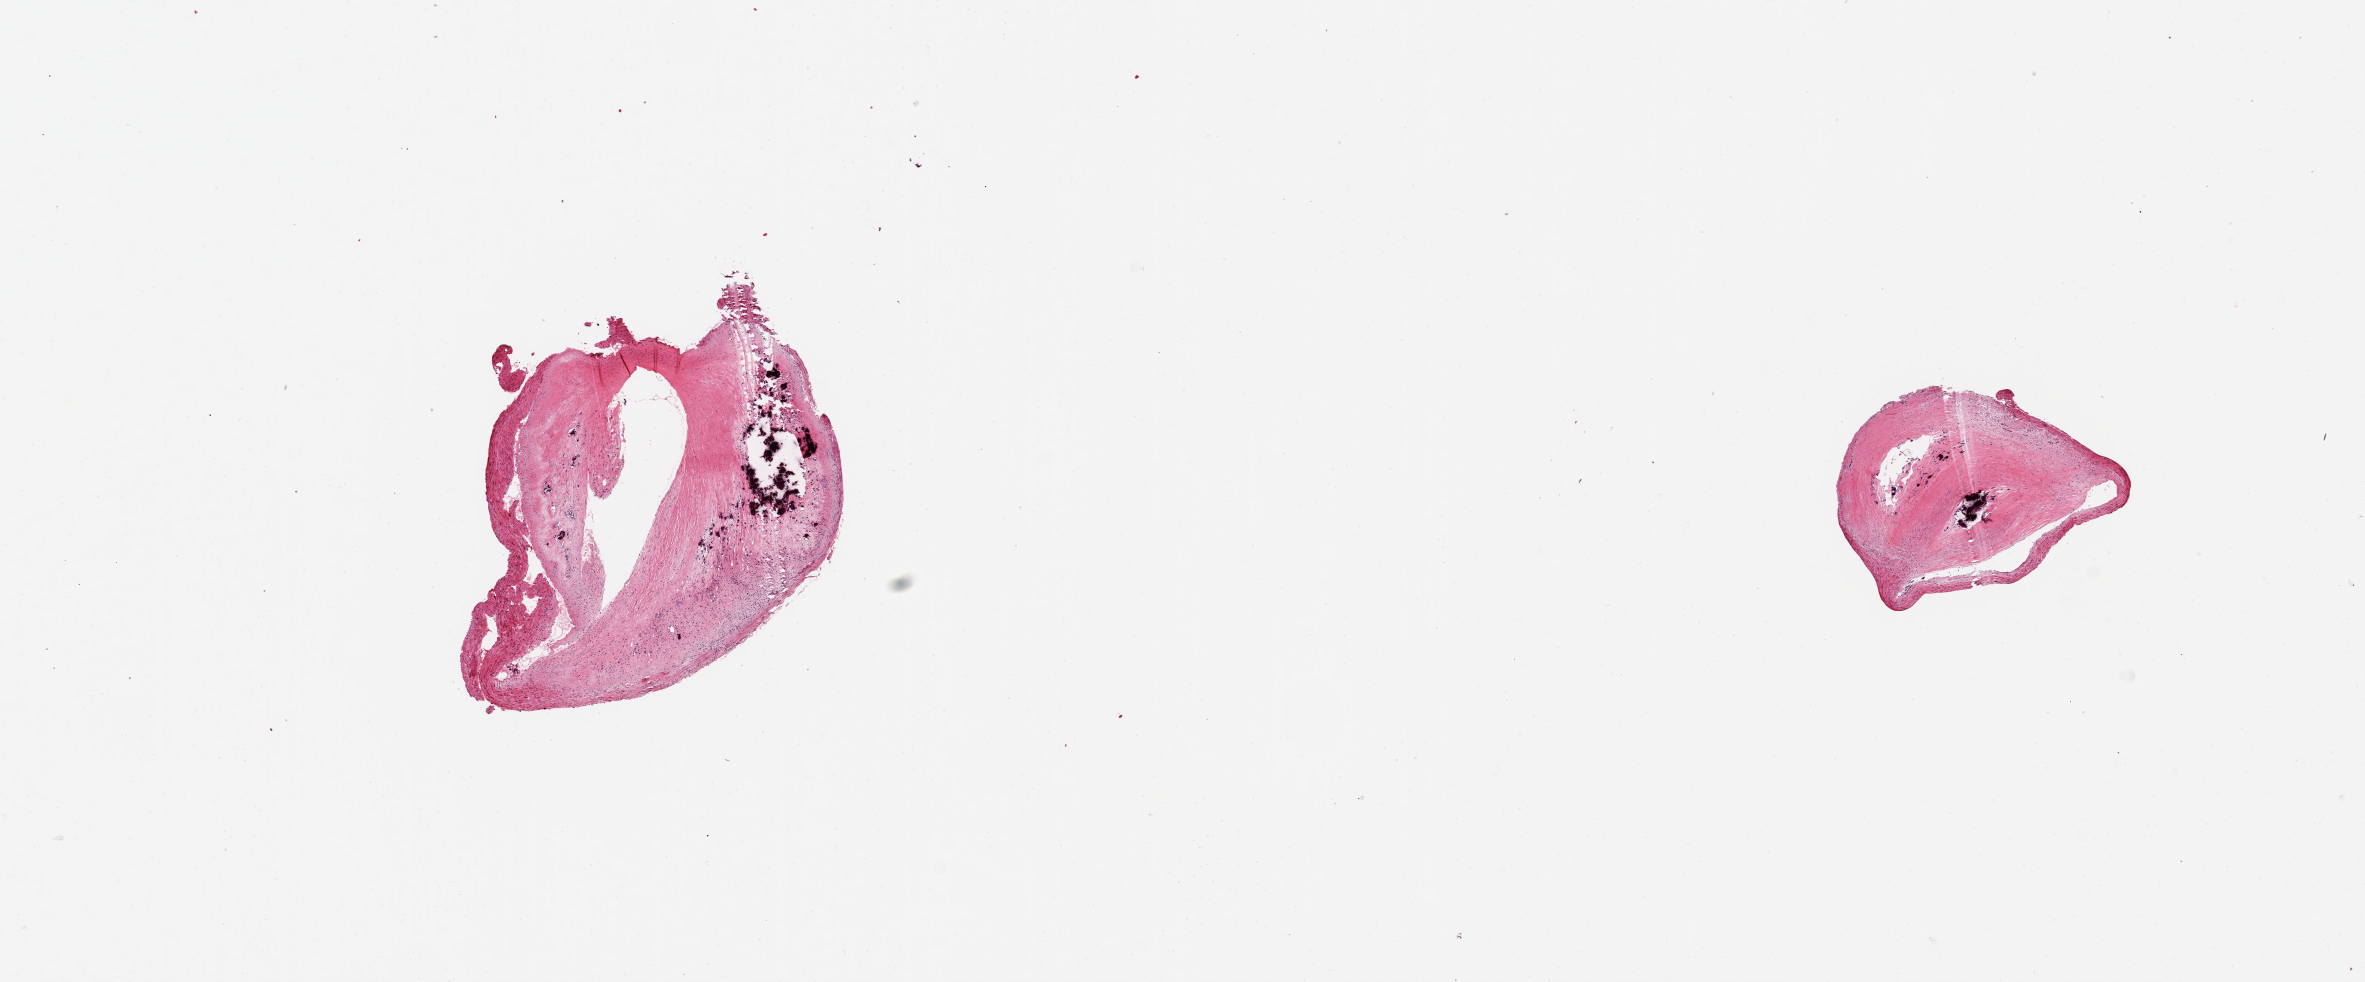
Whole-slide image, H&E stain, a low-resolution overview of the entire scanned area, about 18.7 x 7.8 mm. PAXgene-fixed, paraffin-embedded tissue. Sampled site (target tissue): coronary artery. Tissue donor sample. Female donor.
Review note (as recorded): 2 pieces, 3x3 & 2x2mm; Severe atherosclerosis with calcium; 80% narrowed. Little normal tissue left.